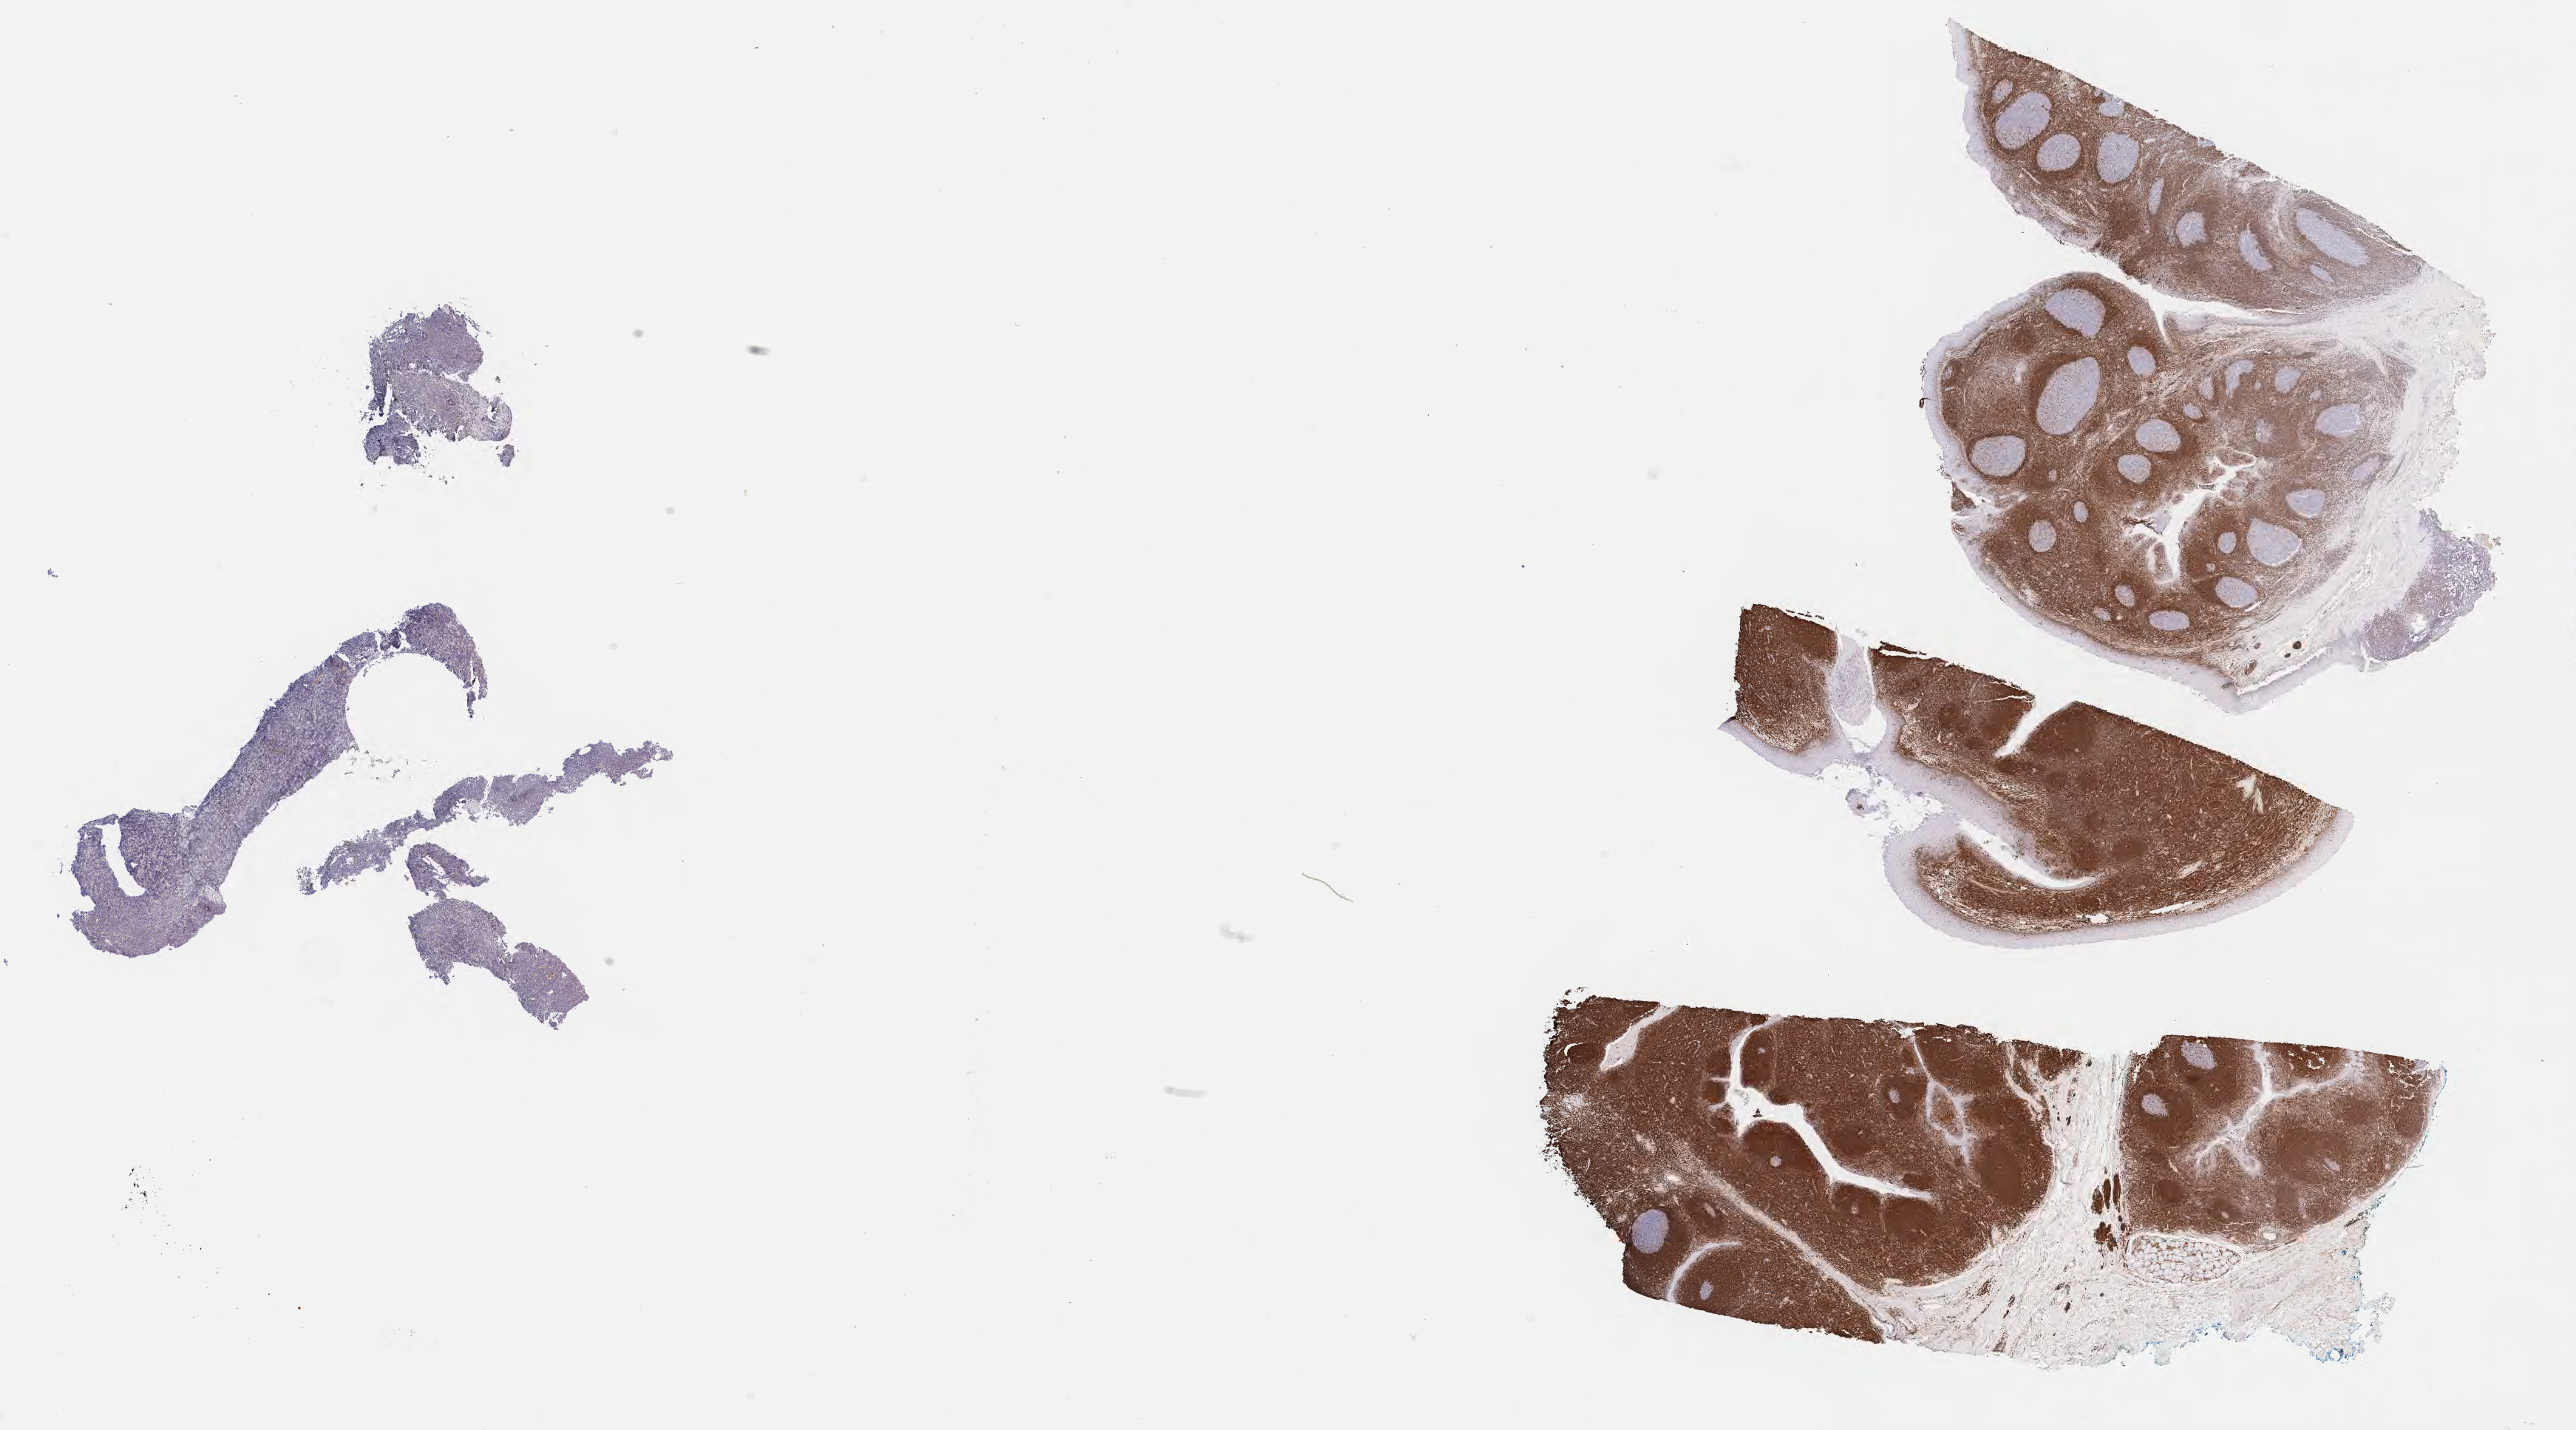
IHC for BCL2, whole-slide image — shown as a low-resolution overview of the whole scanned area (about 28.2 x 15.6 mm); specimen: tumor tissue; site: cranium. Patient: male, age at initial diagnosis 5 years.
Diagnosis: Burkitt lymphoma, NOS.